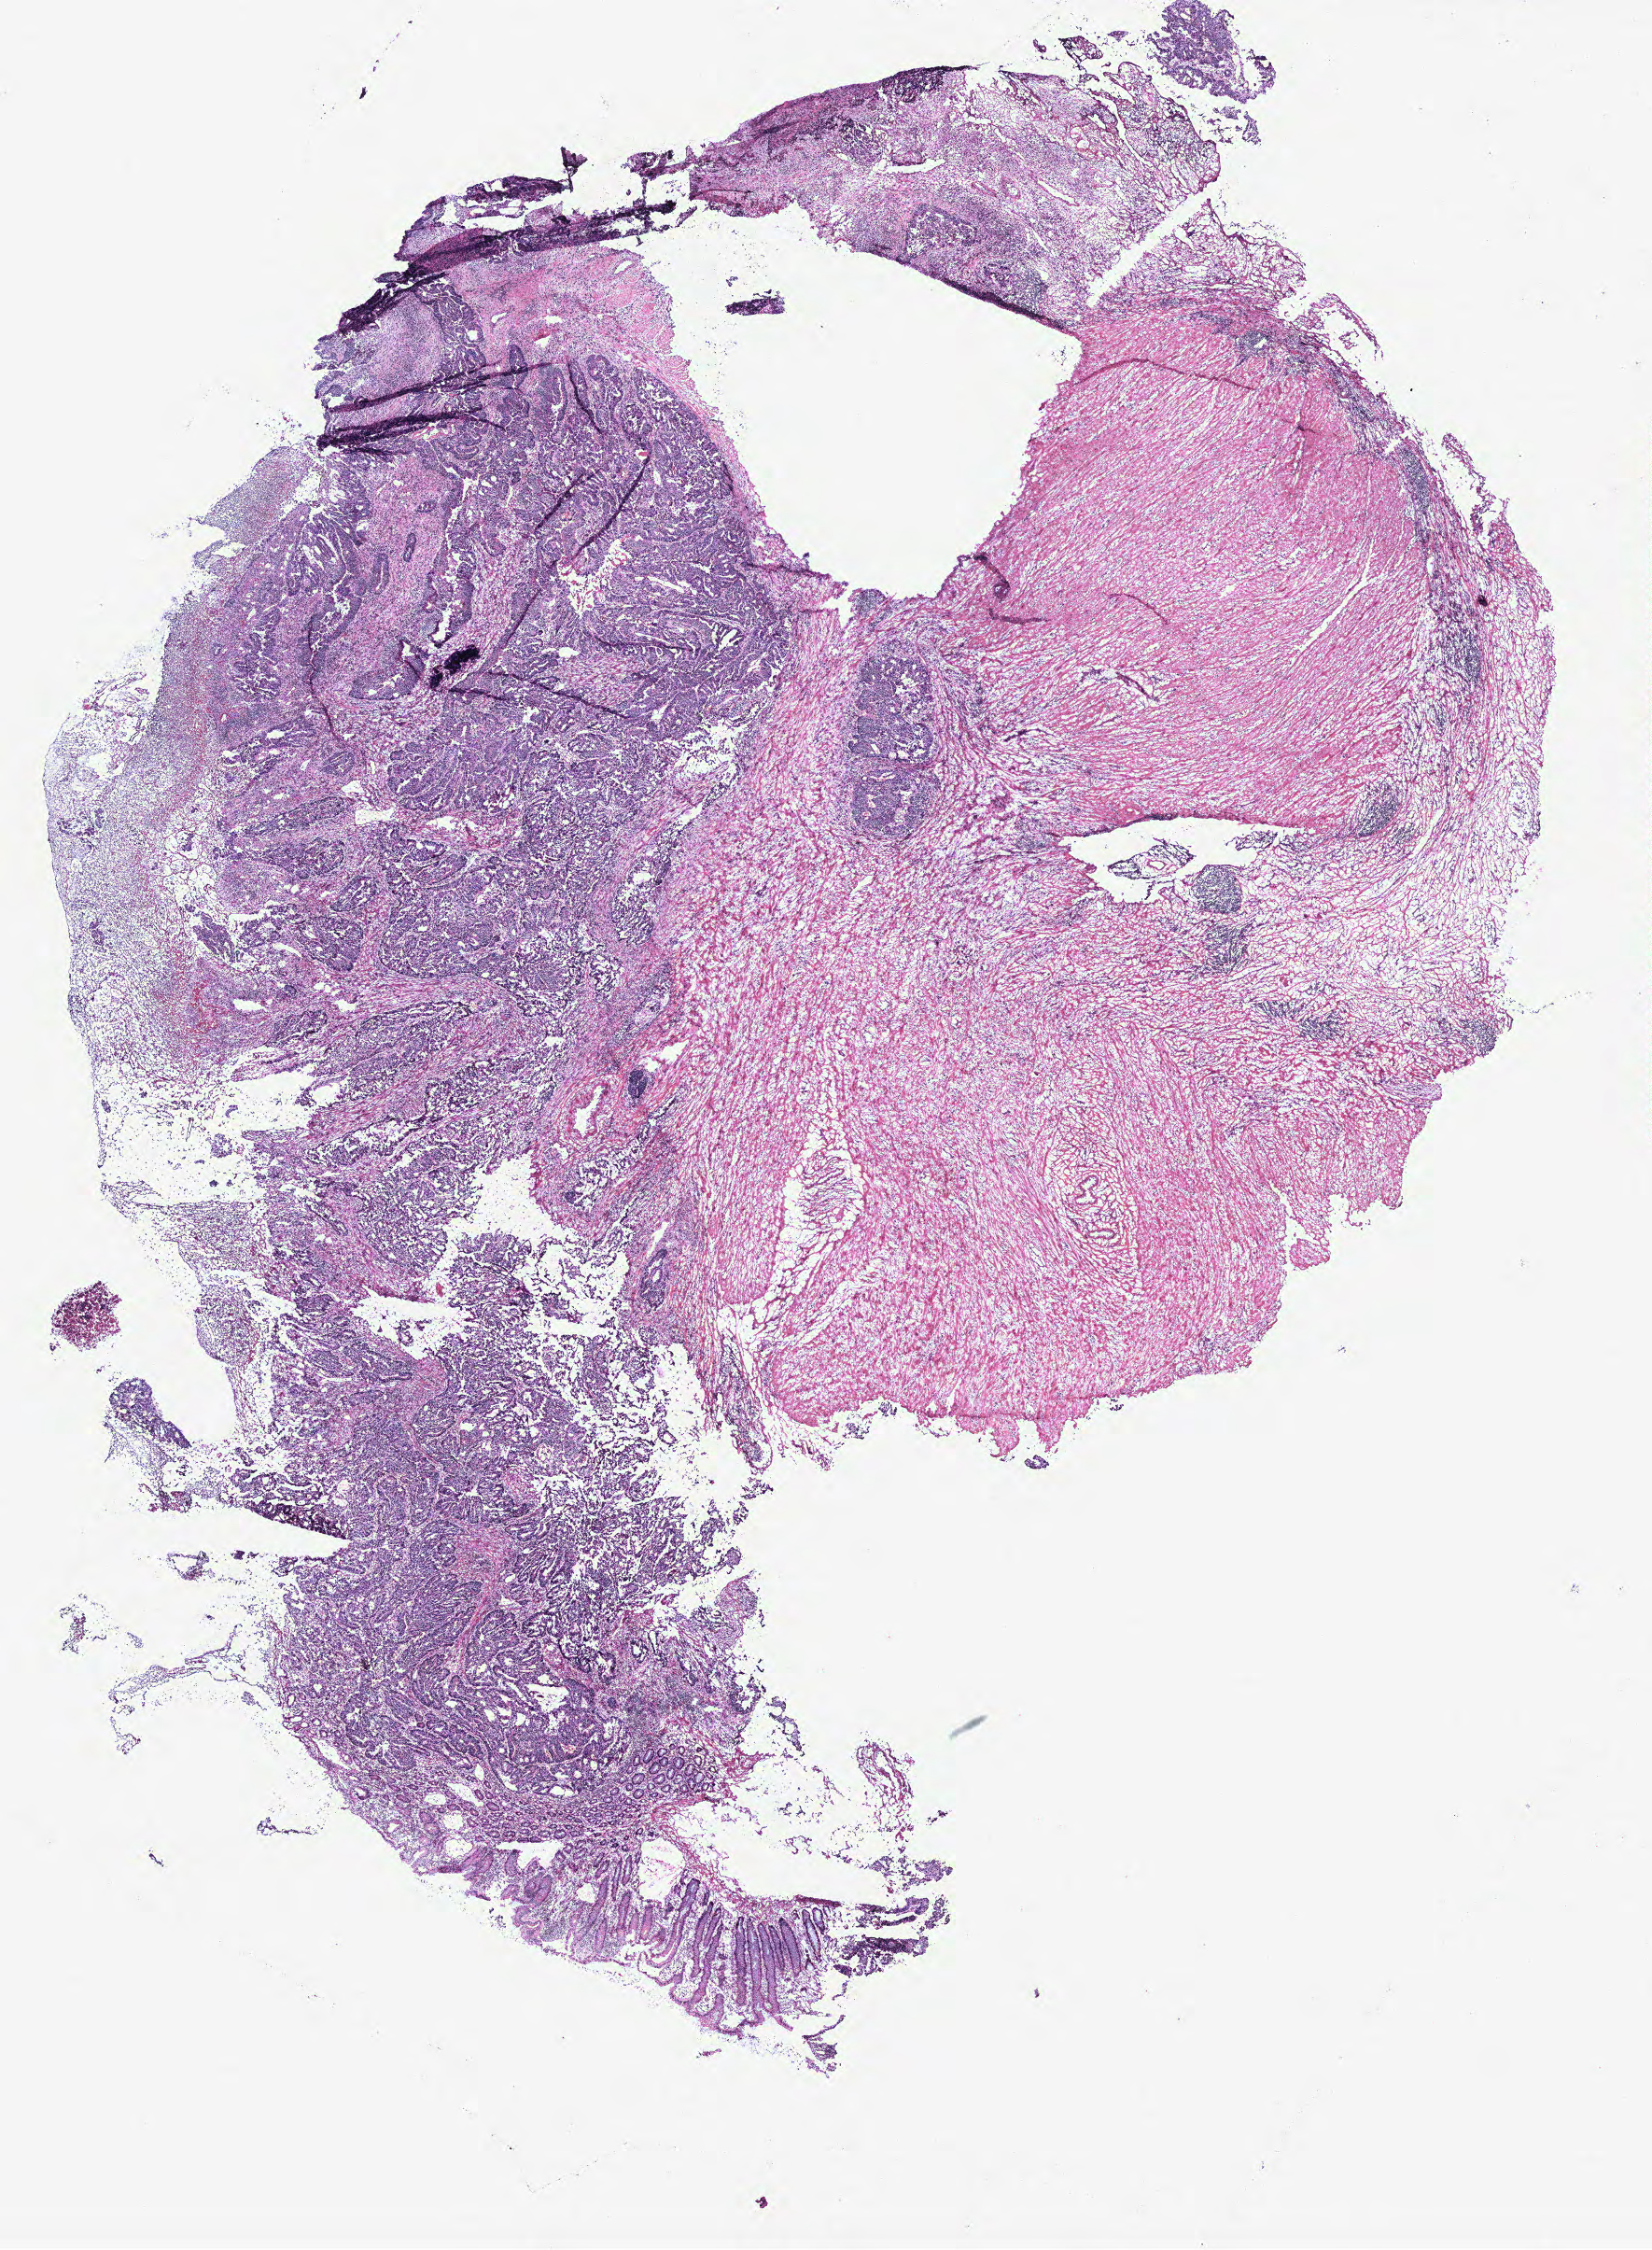
Whole-slide histology image, H&E-stained, shown as a low-resolution overview of the whole scanned area (about 14.2 x 19.3 mm). Colon, tissue type not recorded. Patient sex: male.
Patient diagnosis: Adenocarcinoma, NOS.